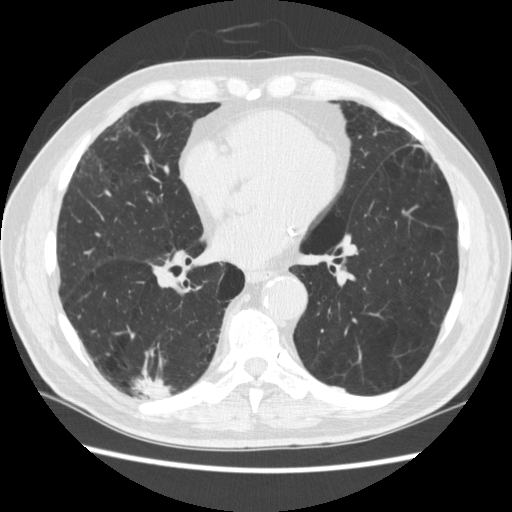
Chest CT (low-dose screening protocol), one axial image, third annual screen, lung window (W 1500 / L -600 HU), 120 kVp, slice 148 of 266 in the series. Male participant, aged 70 years at enrolment. Former smoker at enrolment.
• Expert-annotated lung lesion, box from (x=124, y=360) to (x=183, y=418) px.
• The screening reader recorded 4 non-calcified nodules or masses ≥4 mm on this exam (right lower lobe, right lower lobe, left lower lobe, left lower lobe); which of them this box marks is not recorded.
• Lung cancer was diagnosed 253 days after this screen: squamous cell carcinoma, NOS, right upper lobe, poorly differentiated (G3), stage IV (AJCC 6th edition).